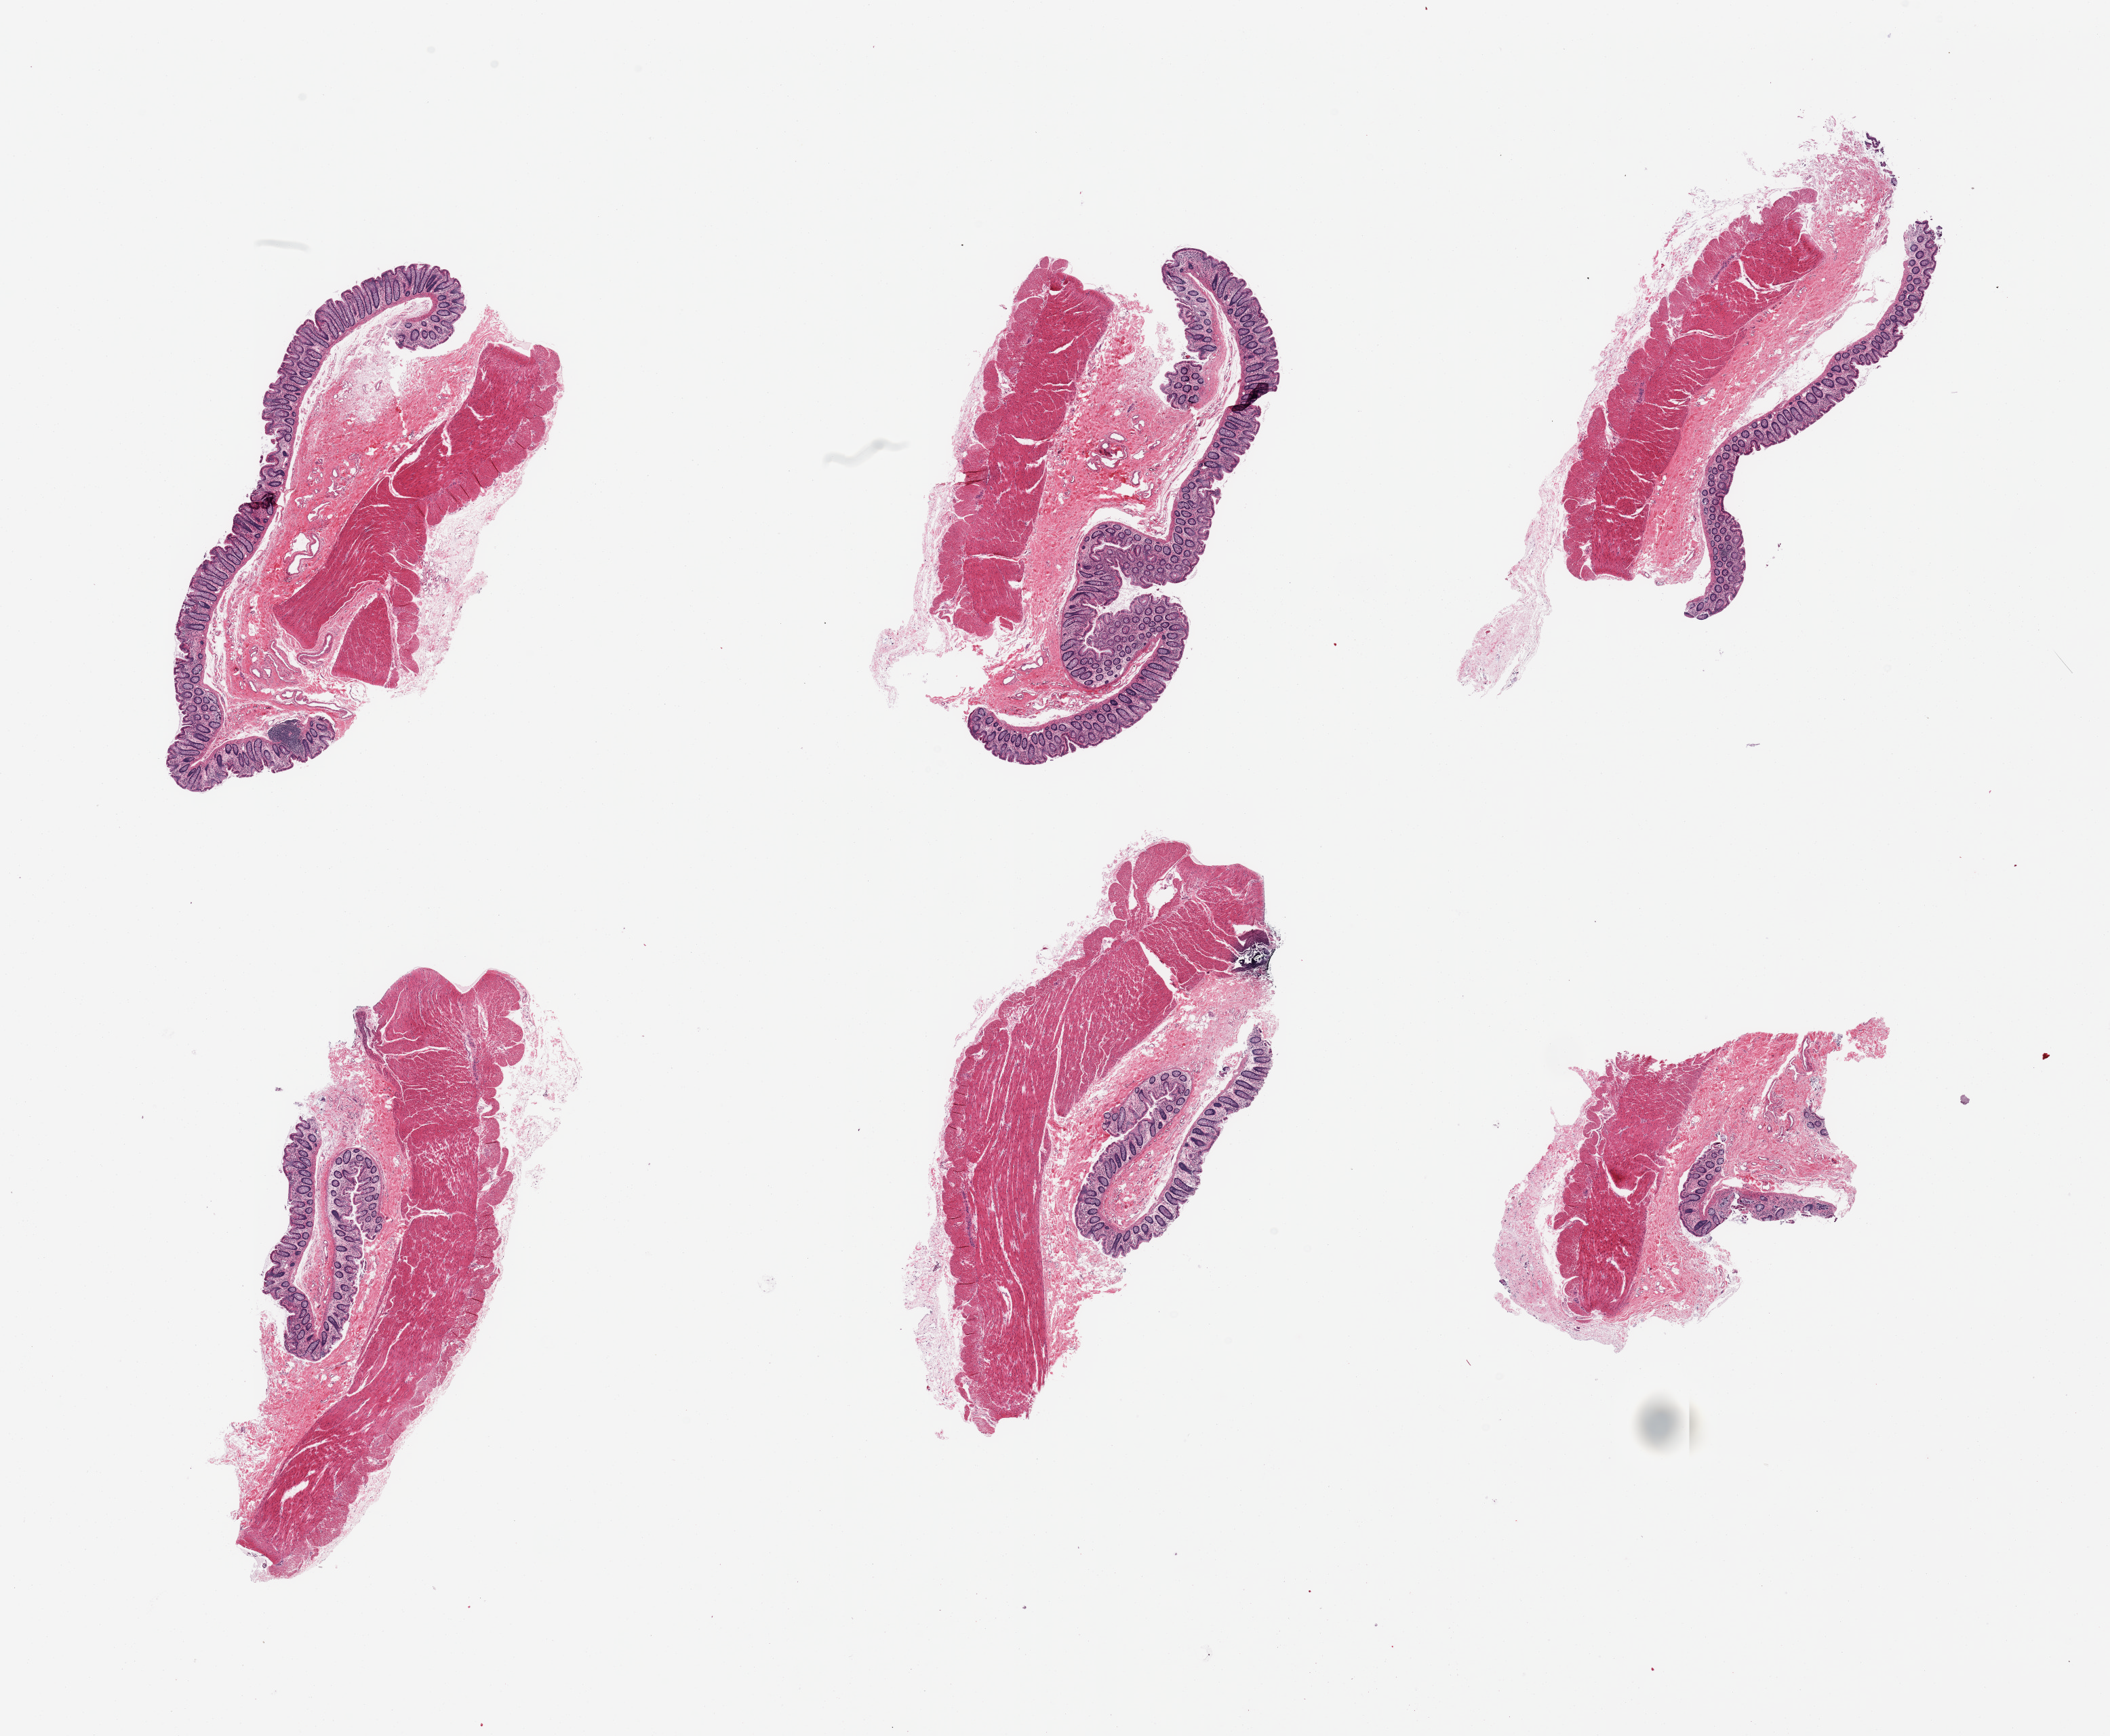
Digitized H&E-stained section — a low-resolution overview of the entire scanned area, about 24.6 x 20.2 mm, PAXgene-fixed, paraffin-embedded tissue, sampled site (target tissue): transverse colon, donor tissue sample. Donor sex: female.
• pathologist's review note for this sample: 6 pieces; mucosa, submucosa, muscularis (variable in composition)